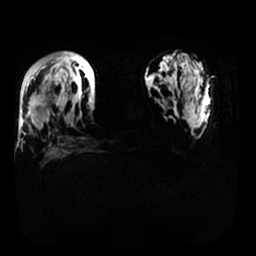
Breast MRI, one axial slice; position 11 of 25 along the scan axis; diffusion-weighted series; image 2 of 4 stored at this slice position (different b-values; order by instance number); 1.5 T; 4 mm slice thickness; 256 × 256 image matrix, field of view 340 × 340 mm. Female patient.
Outlined on this slice (expert manual segmentation):
- tumour on diffusion-weighted imaging: box from (x=32, y=94) to (x=49, y=115) px